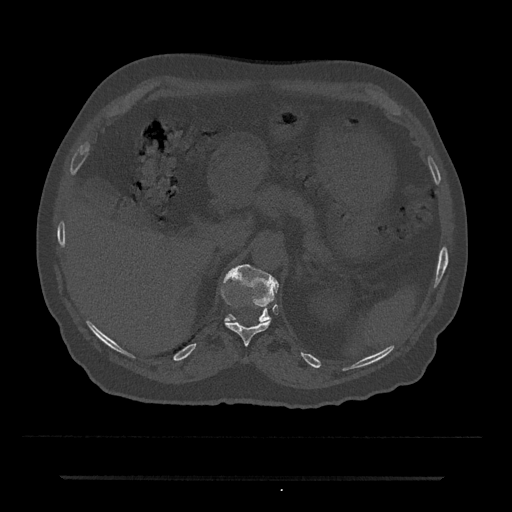
CT including the spine, one axial slice; slice 164 of 797 in the series (ordered by position); reconstruction kernel Br40s/3; bone window (W 1800 / L 400 HU); 0.5 mm slice thickness; 512 × 512 image matrix, field of view 437 × 437 mm. Patient: male, 69 years. From the clinical record (not read from this slice): primary cancer: prostate.
Structures marked on this image (semi-automatically segmented with operator editing):
- T11 vertebra: bounding box [x1, y1, x2, y2] px = [225, 321, 270, 346]
- T12 vertebra: [225, 264, 279, 322]